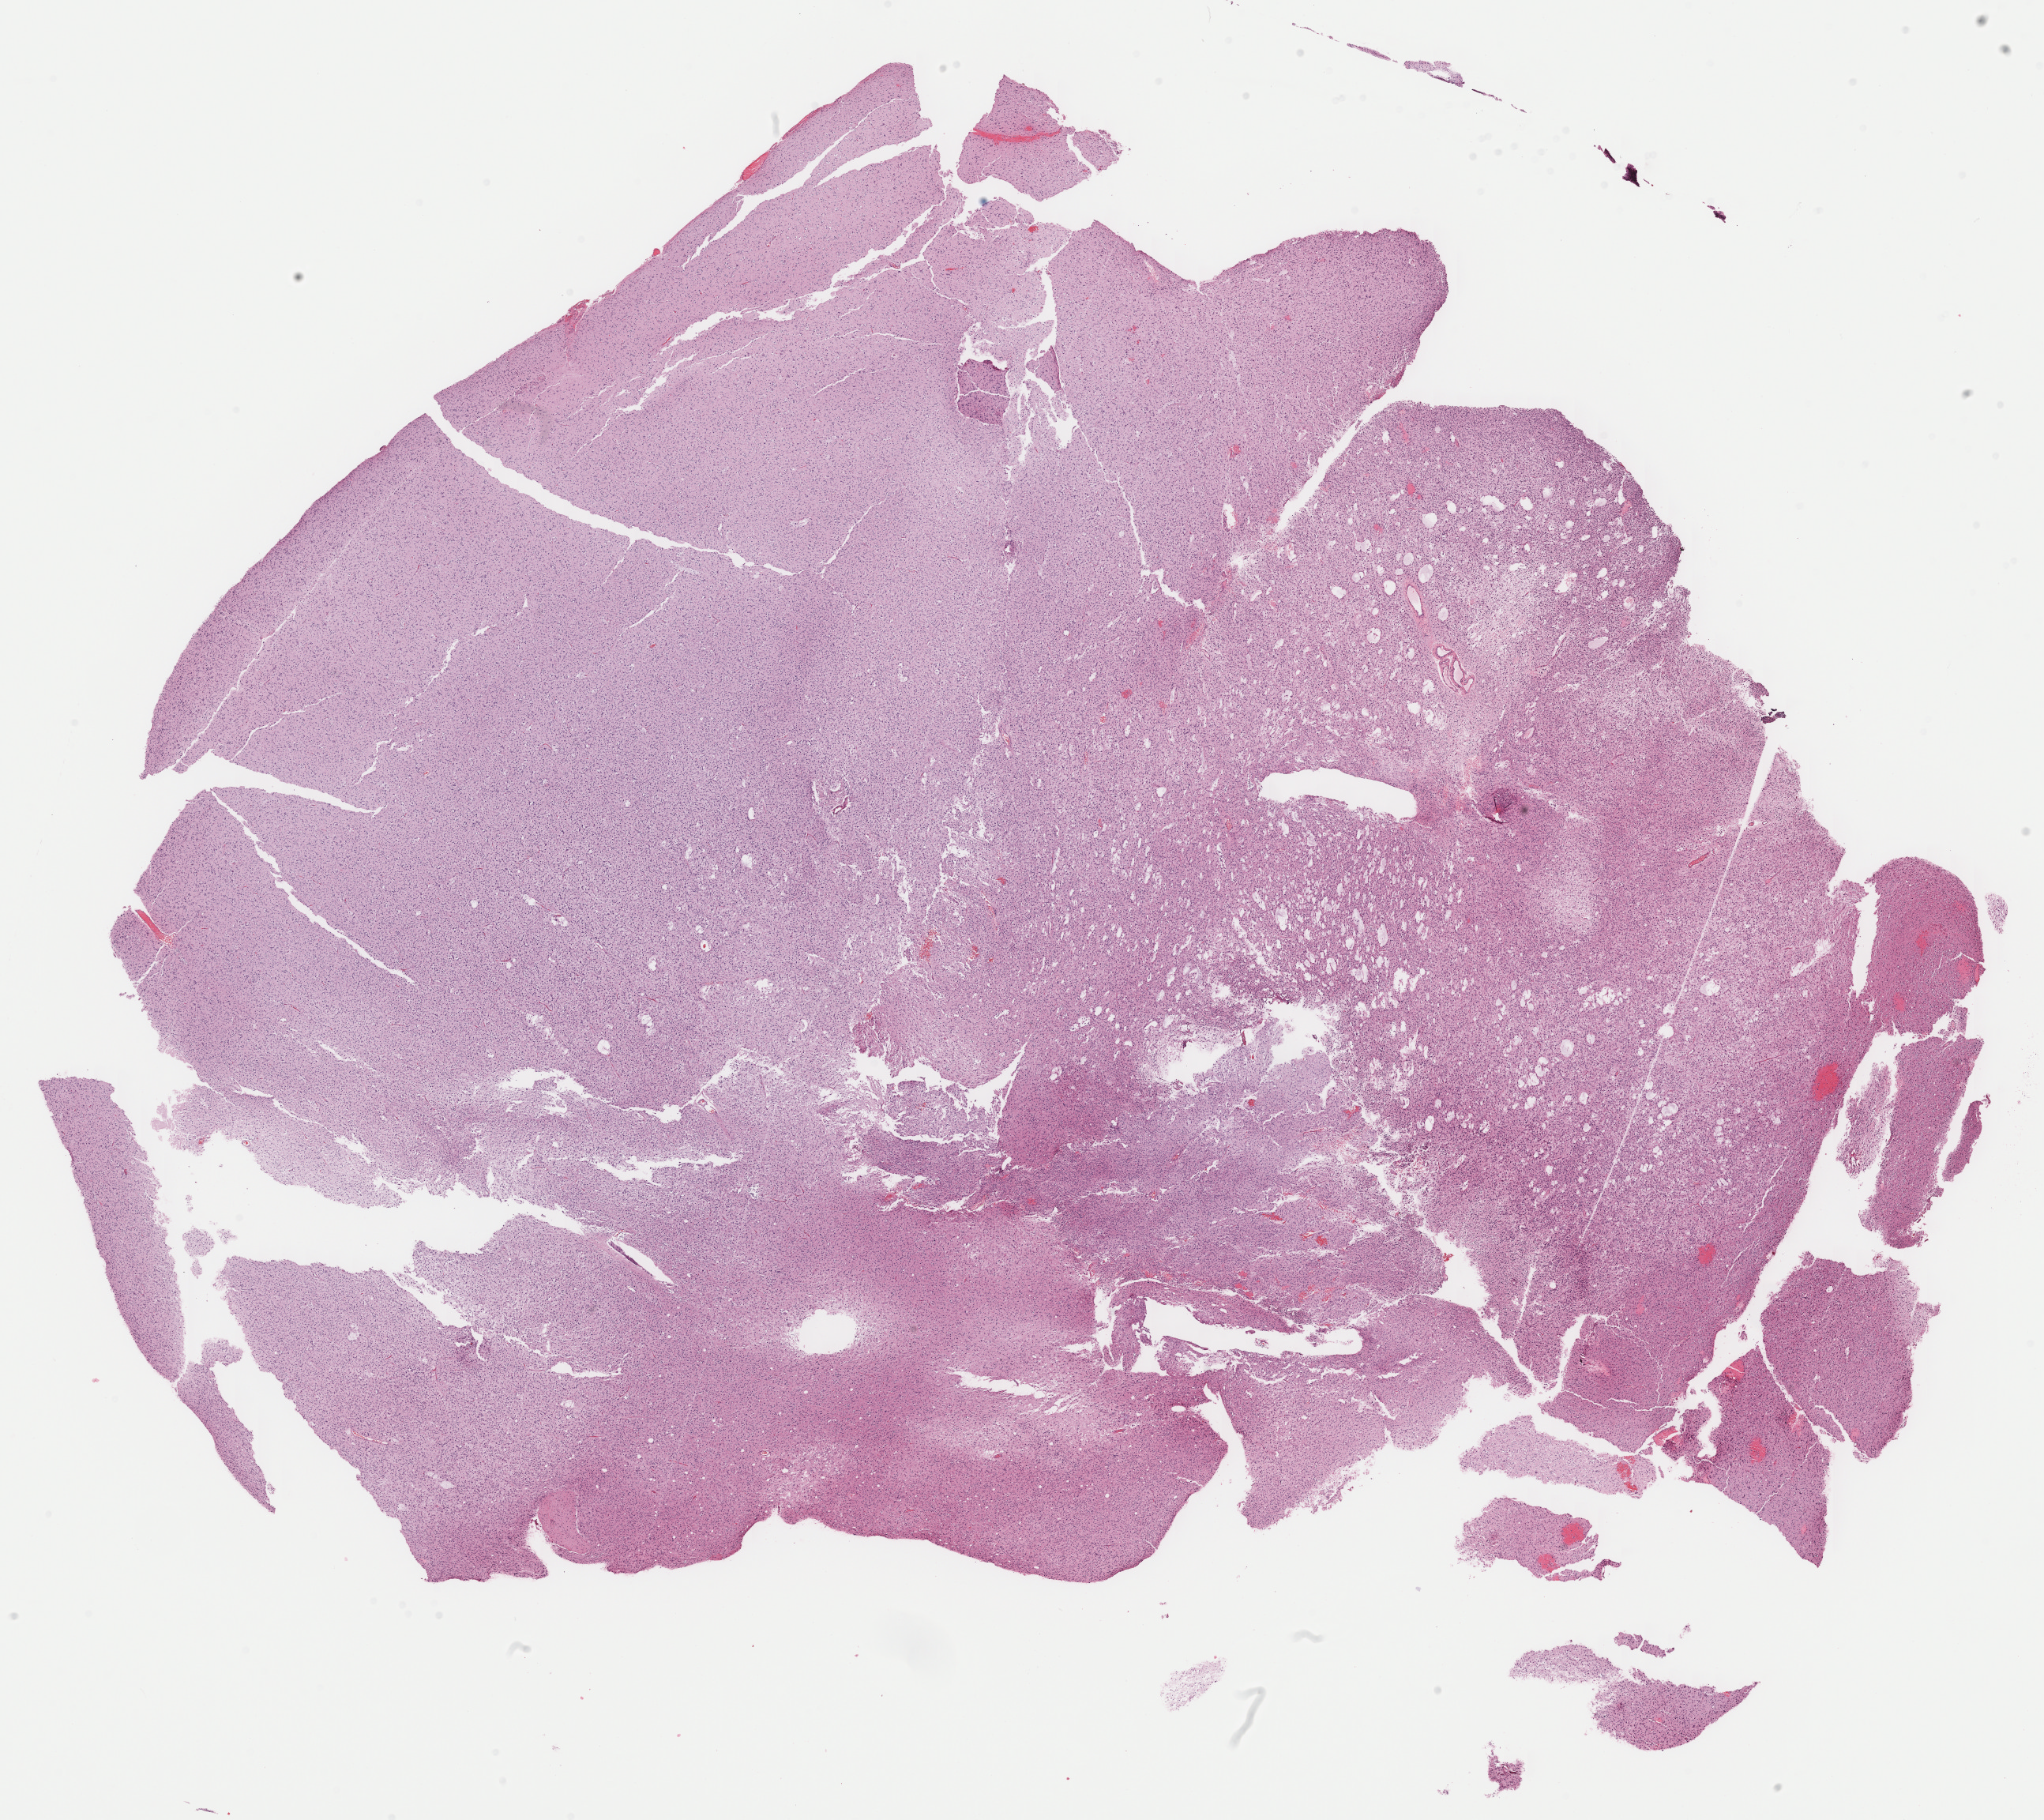
H&E-stained whole-slide image — whole scanned area (about 20.4 x 18.2 mm, from a 40x scan) shown as a low-resolution overview, formalin-fixed paraffin-embedded (FFPE) diagnostic section, brain, primary tumour sample. Female, age 33 years at initial diagnosis. Histologic grade: G2 (moderately differentiated).
Diagnosis: Mixed glioma (temporal lobe). Laterality: left.